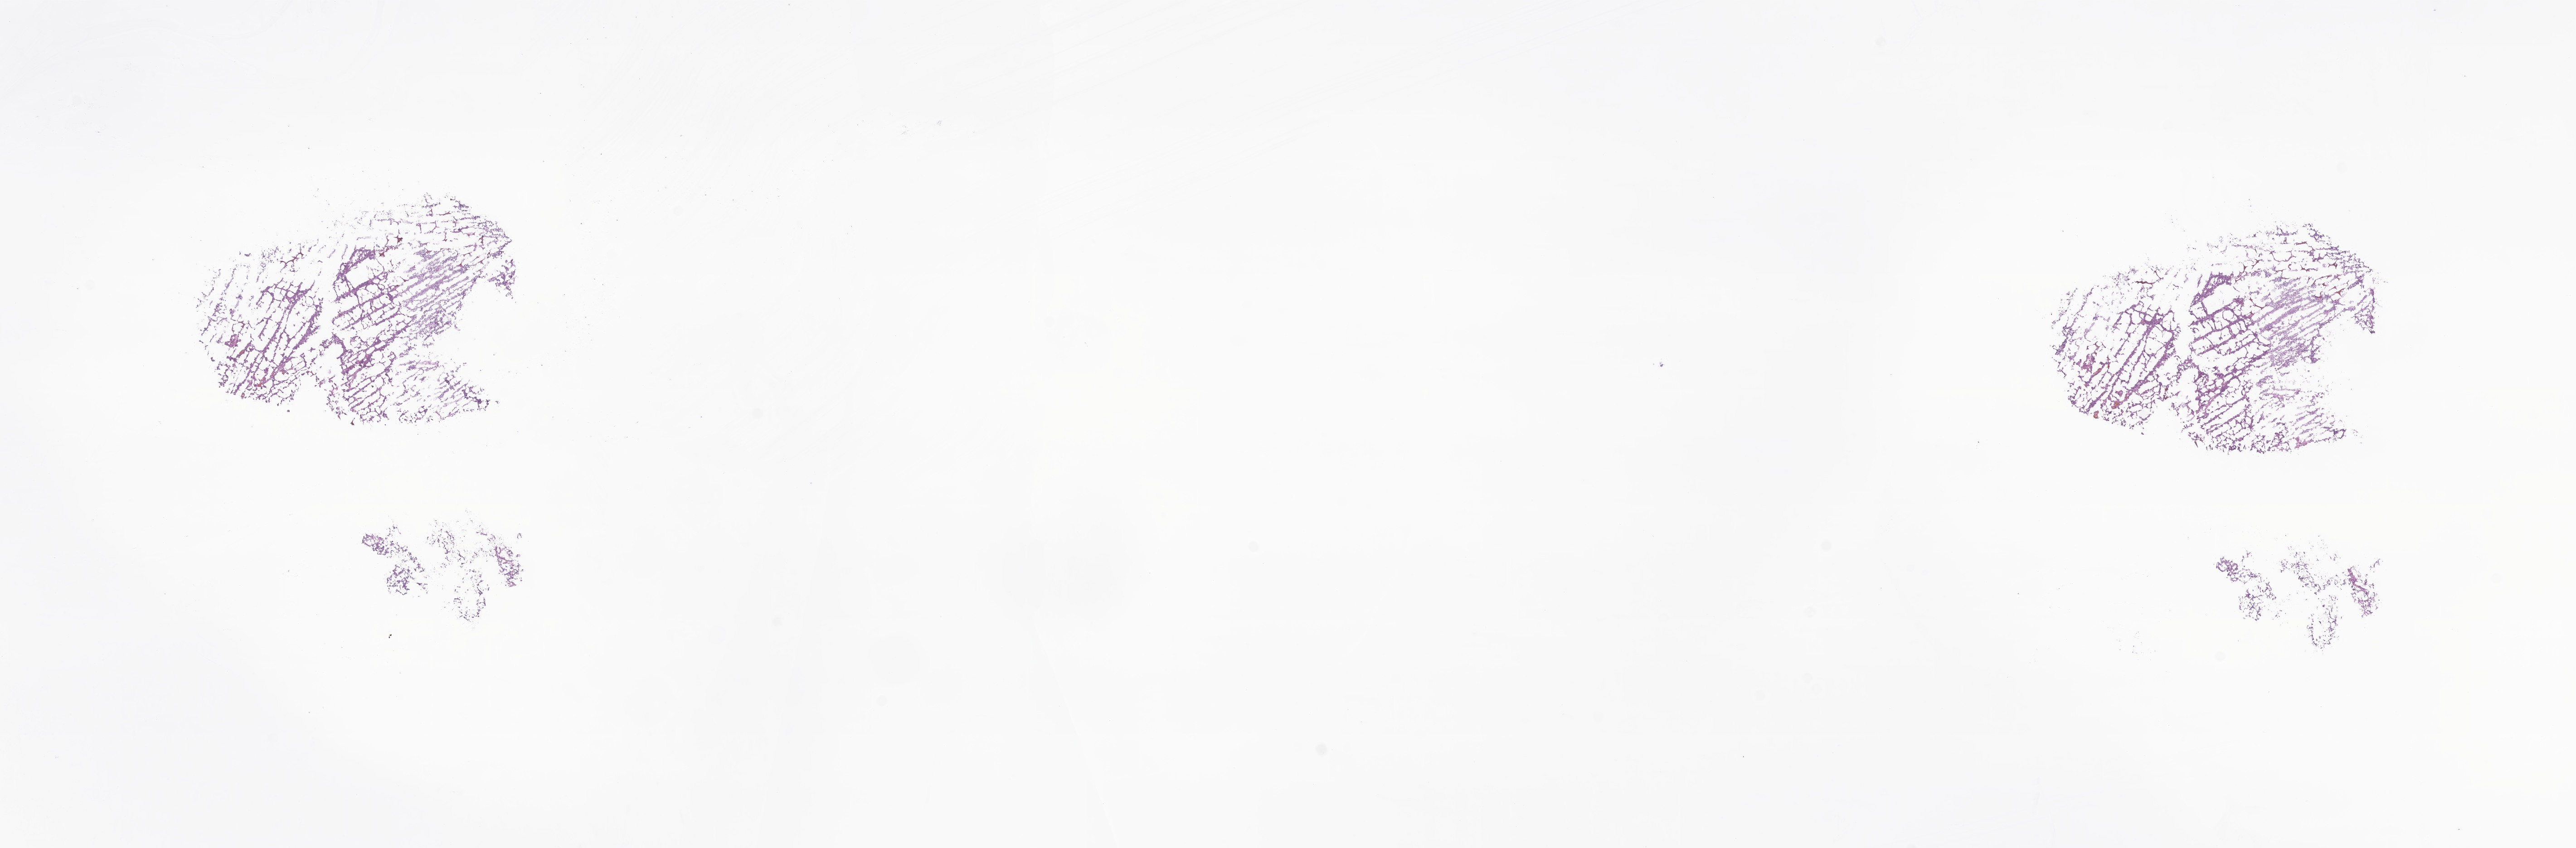
Digitized hematoxylin and eosin (H&E)-stained section of tumor tissue from the brain, whole scanned area (about 24.0 x 7.9 mm) shown as a low-resolution overview, frozen section. Patient: female, age 121 days.
- diagnosis: Atypical teratoid/rhabdoid tumor